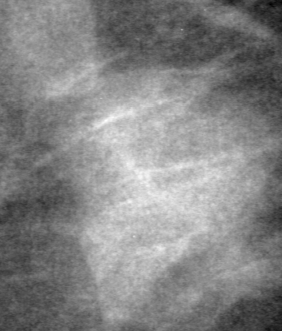
Region of interest cut from a scanned film mammogram (one marked finding); right breast; MLO view.
Finding: mass, shape irregular, margins ill defined; BI-RADS assessment category 4; pathology result (as recorded, not read from the image): benign.